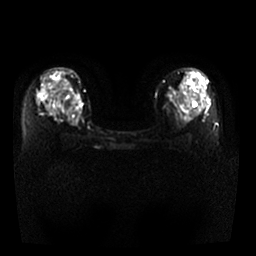
Breast MRI, one axial slice. Slice 19 of 29 in the series (ordered by position). Diffusion-weighted series; image 2 of 4 stored at this slice position (different b-values; order by instance number). 1.5 T. 256 × 256 image matrix, field of view 340 × 340 mm. Female patient.
Outlined on this slice (manually delineated by an expert):
- tumour on diffusion-weighted imaging: box from (x=70, y=95) to (x=79, y=104) px